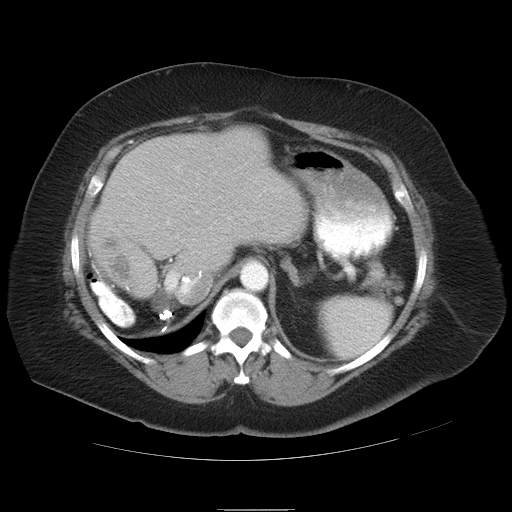
Contrast-enhanced abdominal CT, one axial slice; slice 24 of 37 in the series (ordered by position); reconstruction kernel STANDARD; 120 kVp; intravenous contrast given; soft-tissue window (W 400 / L 40 HU); 7.5 mm slice thickness; 512 × 512 image matrix, field of view 422 × 422 mm. Female patient, age 68 years. Case-level facts recorded for this patient, not image findings: diagnosis: colorectal cancer liver metastases, imaged before liver resection.
Annotated regions visible in this slice (manually delineated by an expert):
- liver: bounding box (x1, y1, x2, y2) in pixels: (89, 128, 309, 302)
- planned liver remnant (the part of the liver to remain after resection): (98, 128, 309, 301)
- portal vein (with intrahepatic branches): (166, 196, 218, 296)
- liver metastasis: (99, 235, 134, 285)